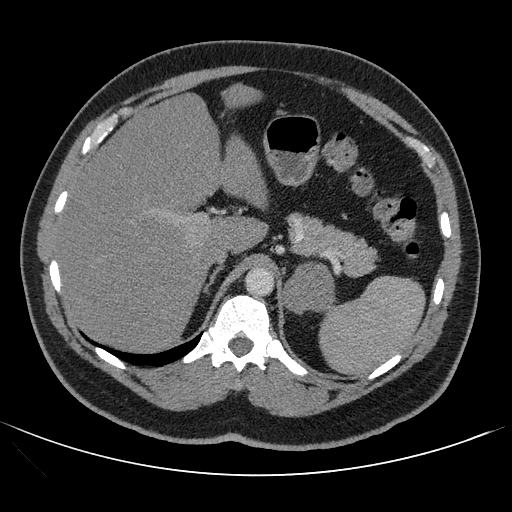
Contrast-enhanced abdominal CT, one axial slice. Slice 77 of 121 in the series (ordered by position). 120 kVp. Intravenous contrast given. Soft-tissue window (W 400 / L 40 HU). 512 × 512 image matrix. Patient: male, 53 years. Case-level facts recorded for this patient, not image findings: diagnosis: adrenocortical carcinoma; tumour side: left adrenal; tumour size at pathology: 7.9 cm; Ki-67 index: 20 %; stage (as recorded): 2.
Outlined on this slice (semi-automatic segmentation, software-assisted and operator-edited):
- mass: bounding box (x1, y1, x2, y2) in pixels: (284, 263, 334, 312)